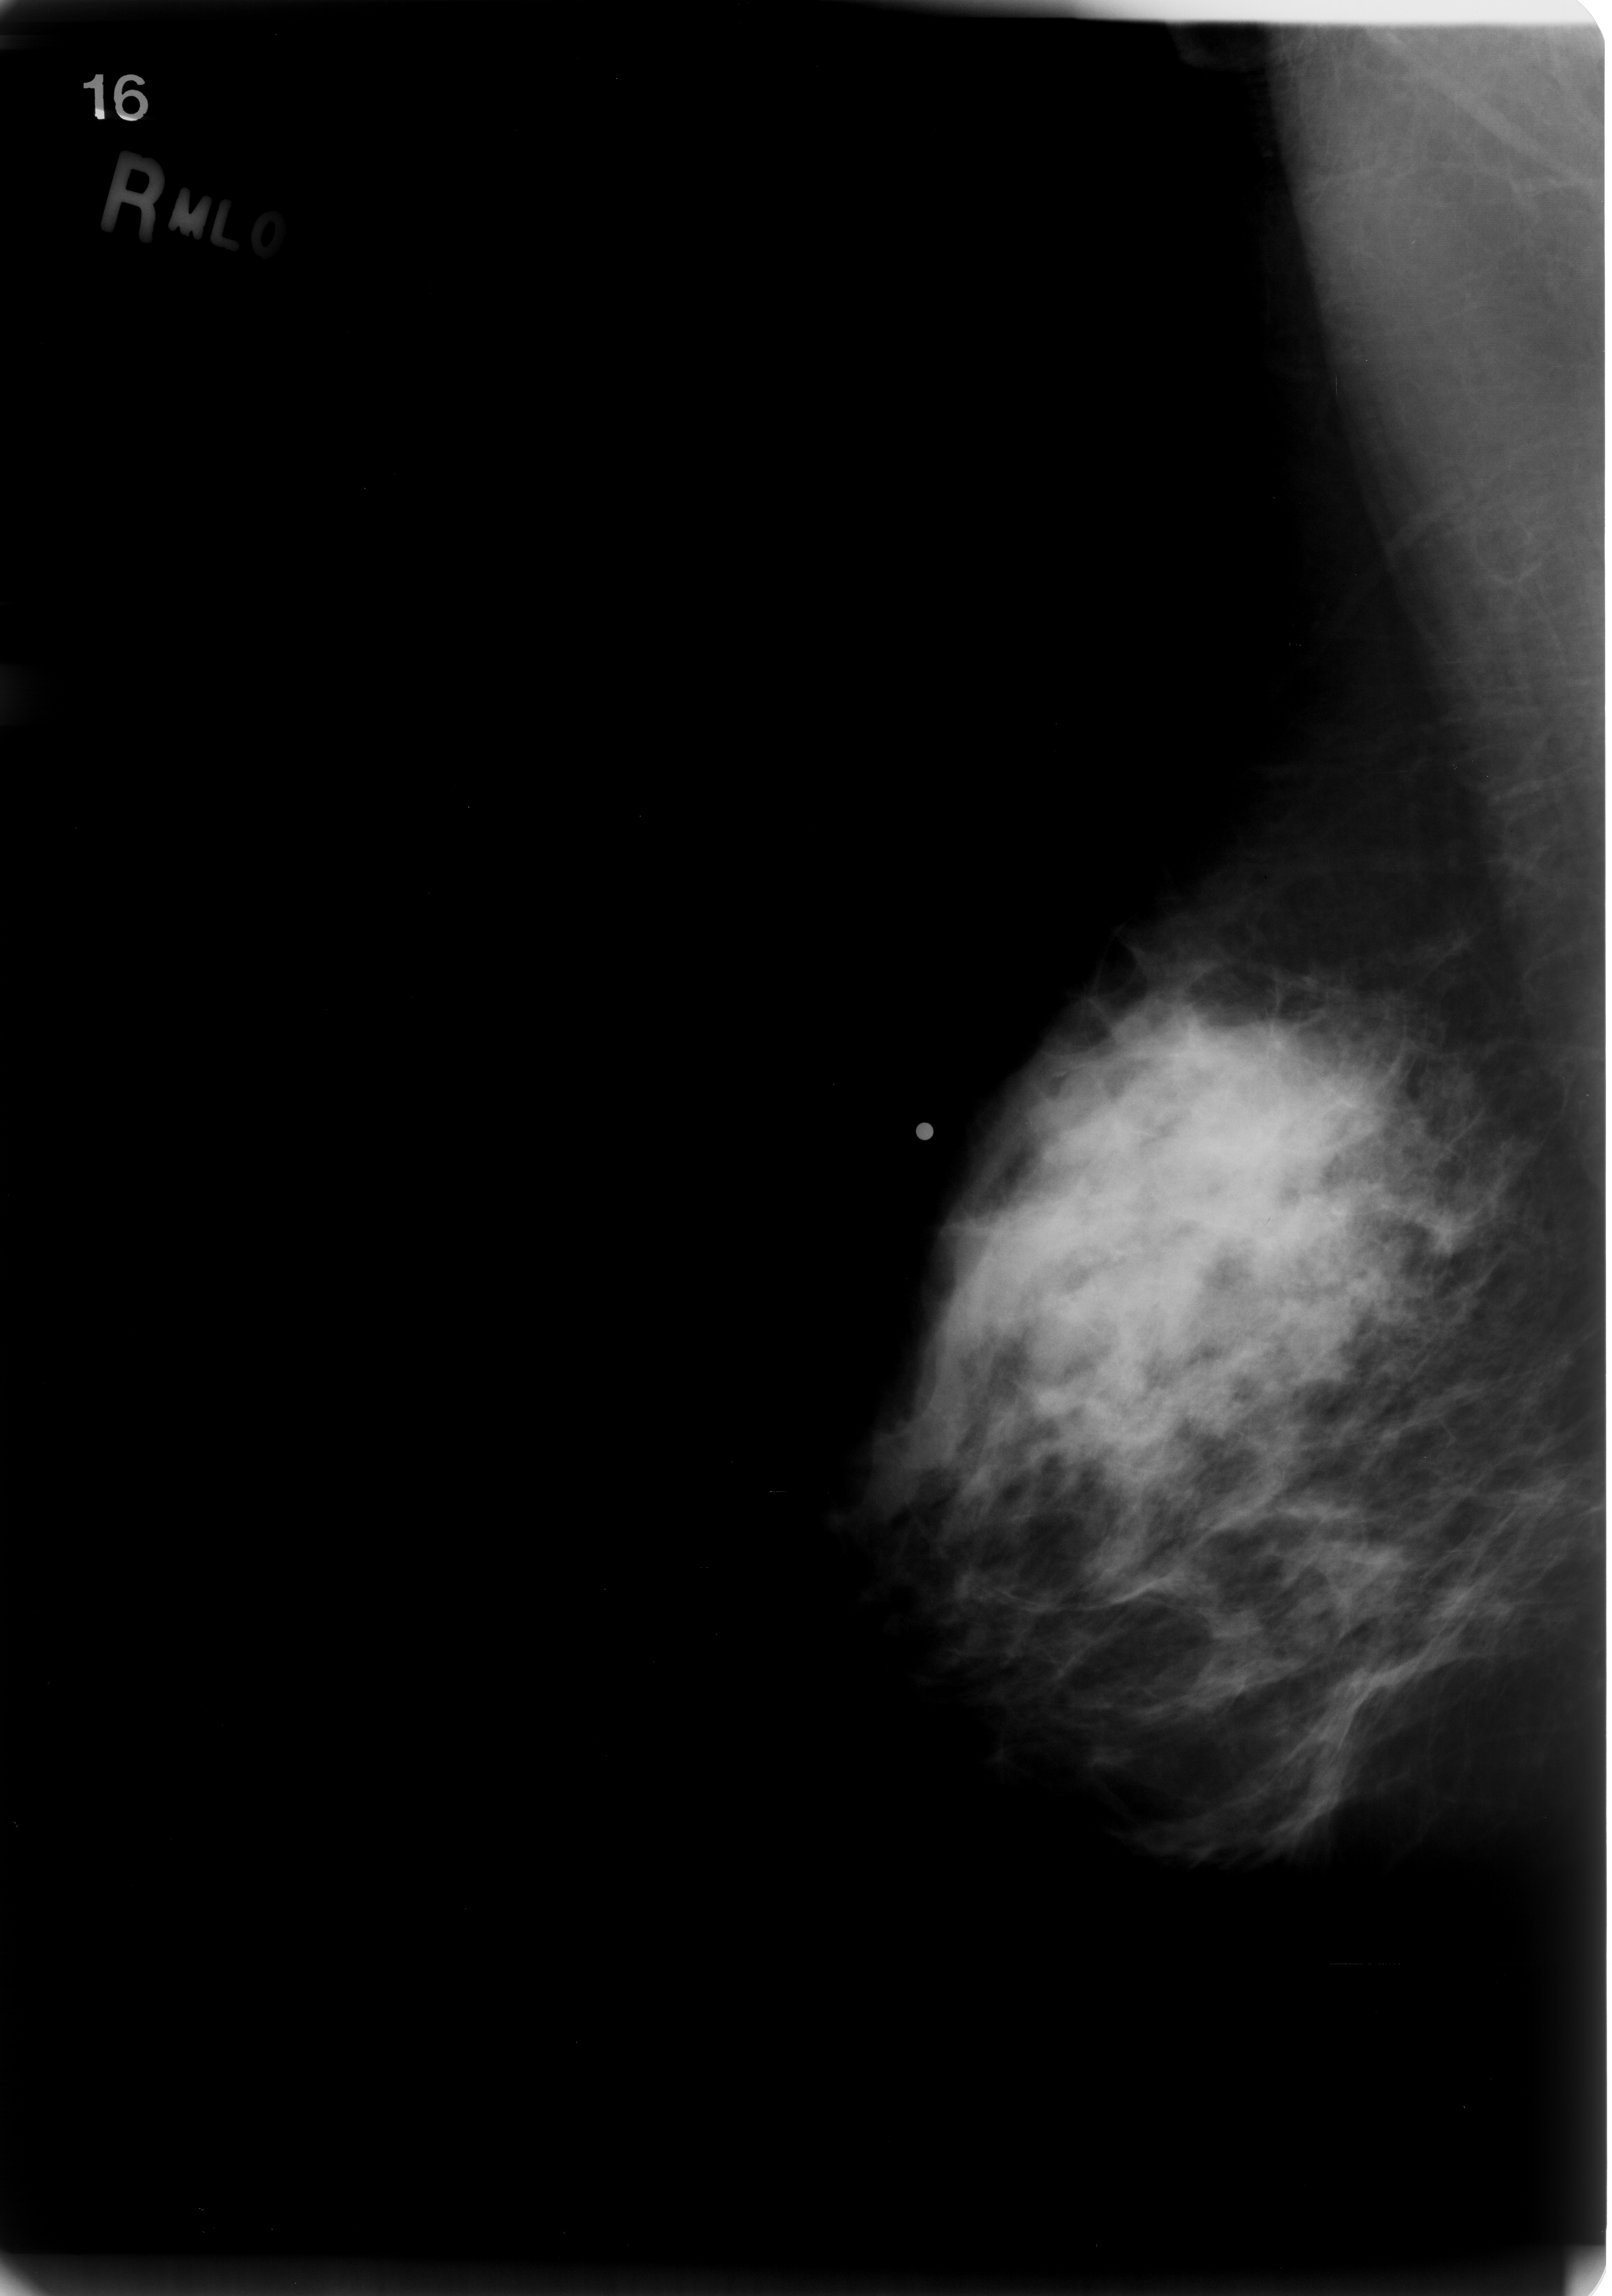
Digitized screen-film mammogram; right breast; MLO view; breast composition: scattered fibroglandular densities (BI-RADS density category 2 of 4).
Mass, shape asymmetric breast tissue, margins ill defined; BI-RADS assessment category 5; subtlety rating 5 on a 1 (subtle) to 5 (obvious) scale; pathology (as recorded): malignant.